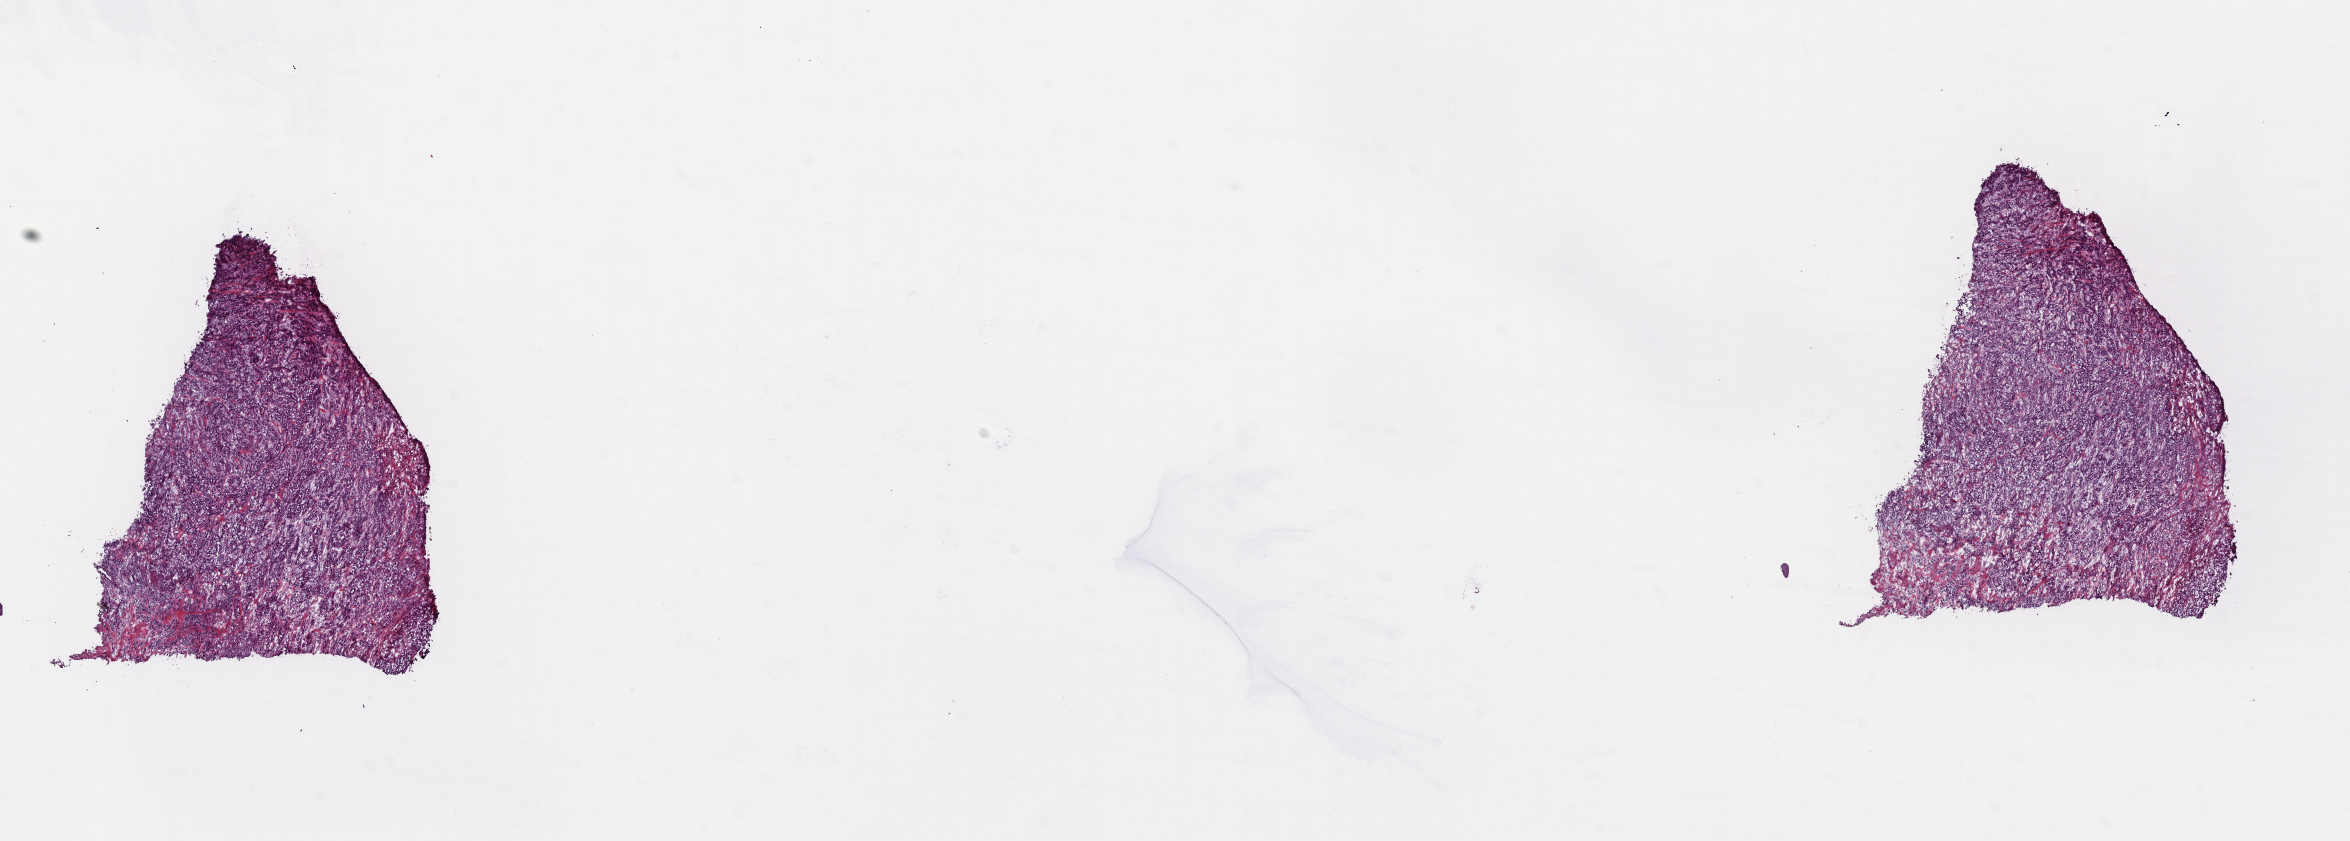
Digitized Hematoxylin and eosin (H&E) stained tissue section (whole slide), shown as a low-resolution overview of the whole scanned area (about 18.5 x 6.6 mm, slide scanned at 40x); frozen section from the top of the tissue portion; sample: primary tumour, lung. Female, age 69 years at initial diagnosis. Composition of this section per pathologist review: tumour cells 50%, tumour nuclei 75%, normal cells 0%, stromal cells 42%, necrosis 8%. Inflammatory infiltration, as recorded: lymphocyte infiltration 10%, monocyte infiltration 3%, neutrophil infiltration 3%.
TNM: T2 N1 M0. Diagnosis: Squamous cell carcinoma, NOS. AJCC pathologic stage: IIB (6th edition).